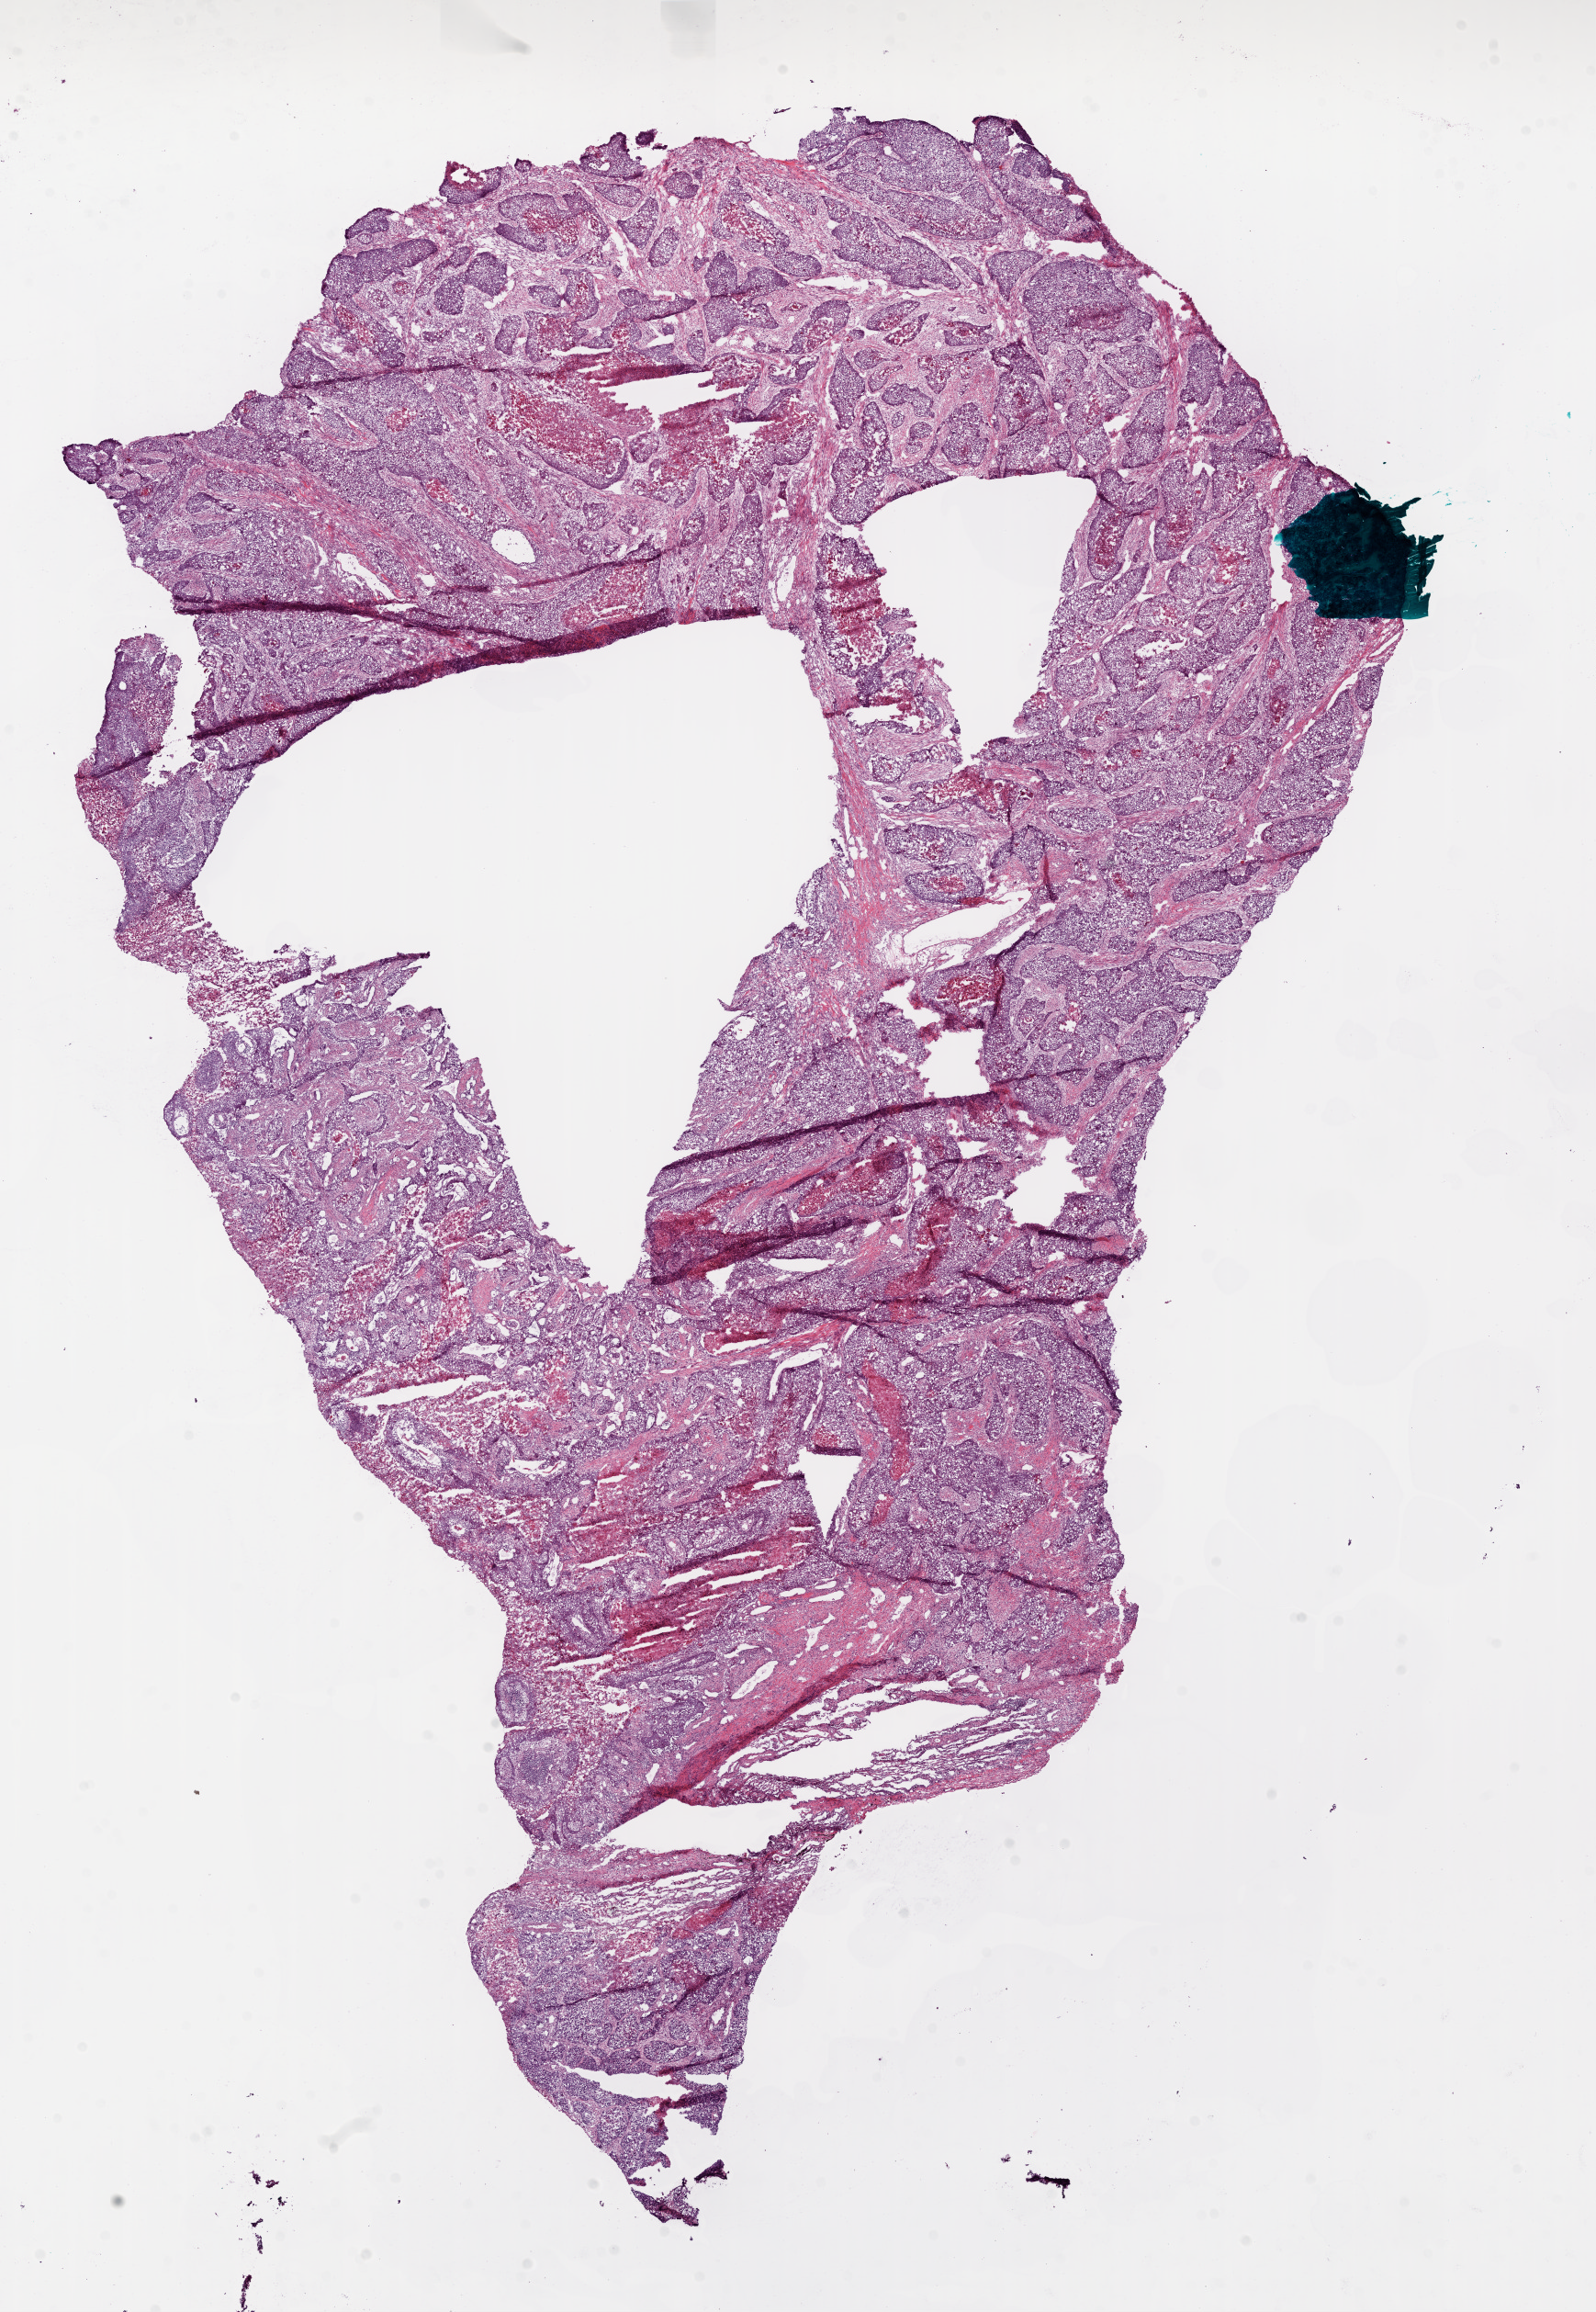
Digitized H&E tissue section (whole slide), low-resolution overview of the scanned area, about 14.0 x 20.3 mm (slide scanned at 20x); frozen section from the bottom of the tissue portion; sample: primary tumour, lung. Male, age 69 years at initial diagnosis. Composition of this section per pathologist review: tumour nuclei 95%, necrosis 10%.
• histologic diagnosis: Squamous cell carcinoma, NOS (lower lobe, lung)
• AJCC pathologic stage: IIB